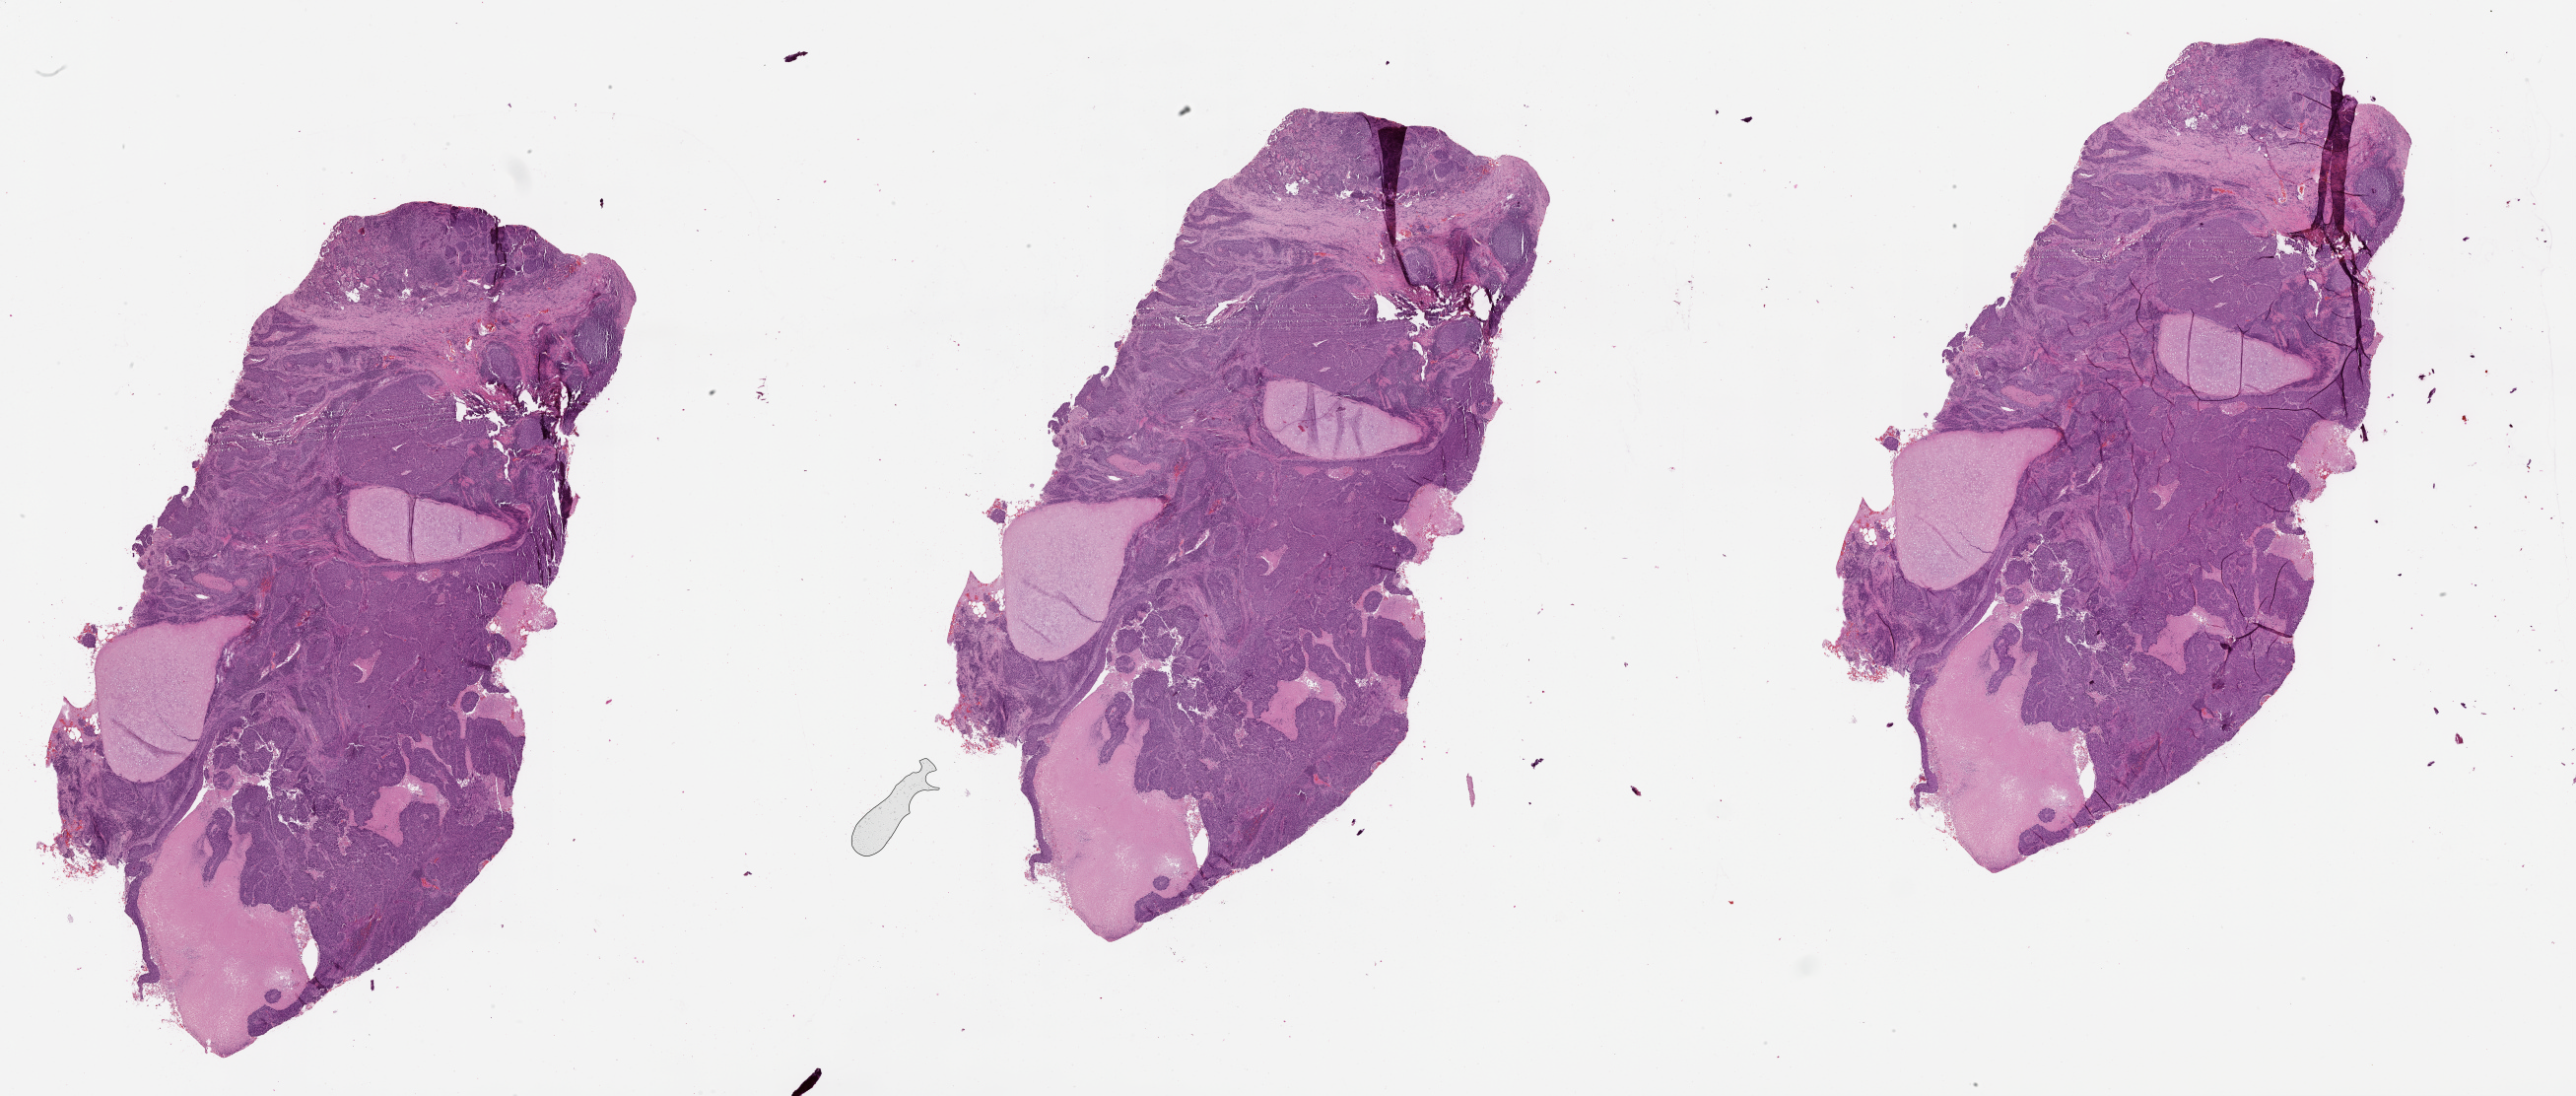
Digitized H&E-stained tissue section (whole slide) — shown as a low-resolution overview of the whole scanned area (about 42.1 x 17.9 mm). Lung, tumour tissue. Male, 58 y/o.
Patient diagnosis (cohort enrolment): squamous cell carcinoma (lung).